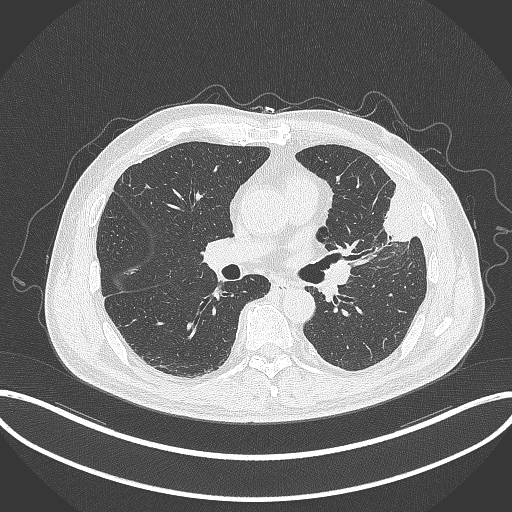
Chest CT, one axial slice; position 179 of 382 along the scan axis; reconstruction kernel B70f; lung window (W 1500 / L -600 HU); 512 × 512 image matrix, field of view 415 × 415 mm. Patient: male, 64 years. Case-level facts recorded for this patient, not image findings: clinical TNM (as recorded): T4 N1 M0; histopathological grade: G3.
Annotated regions visible in this slice (rectangle marked by the reading radiologist):
- lung tumour (recorded histology: adenocarcinoma): bounding box [x1, y1, x2, y2] px = [373, 178, 422, 249]